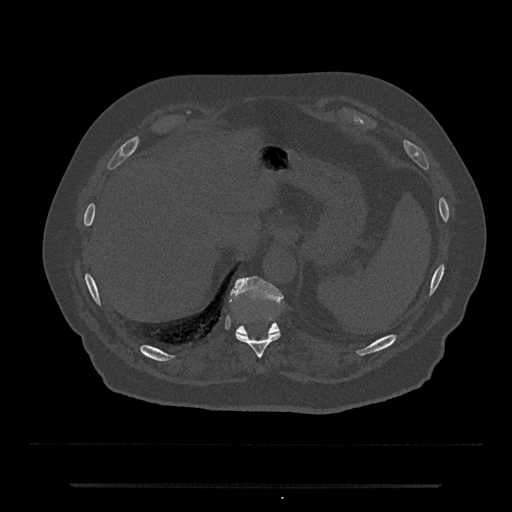
CT including the spine, one axial slice; position 686 of 797 along the scan axis; reconstruction kernel Br40s/3; bone window (W 1800 / L 400 HU); 512 × 512 image matrix, field of view 434 × 434 mm. Patient: male, 80 years. Case-level facts recorded for this patient, not image findings: primary cancer: prostate; vertebrae with lytic lesions (as recorded): L1, T11.
Outlined on this slice (semi-automatically segmented with operator editing):
- T10 vertebra: box from (x=236, y=331) to (x=281, y=358) px
- T11 vertebra: (x=230, y=276)–(x=283, y=335)